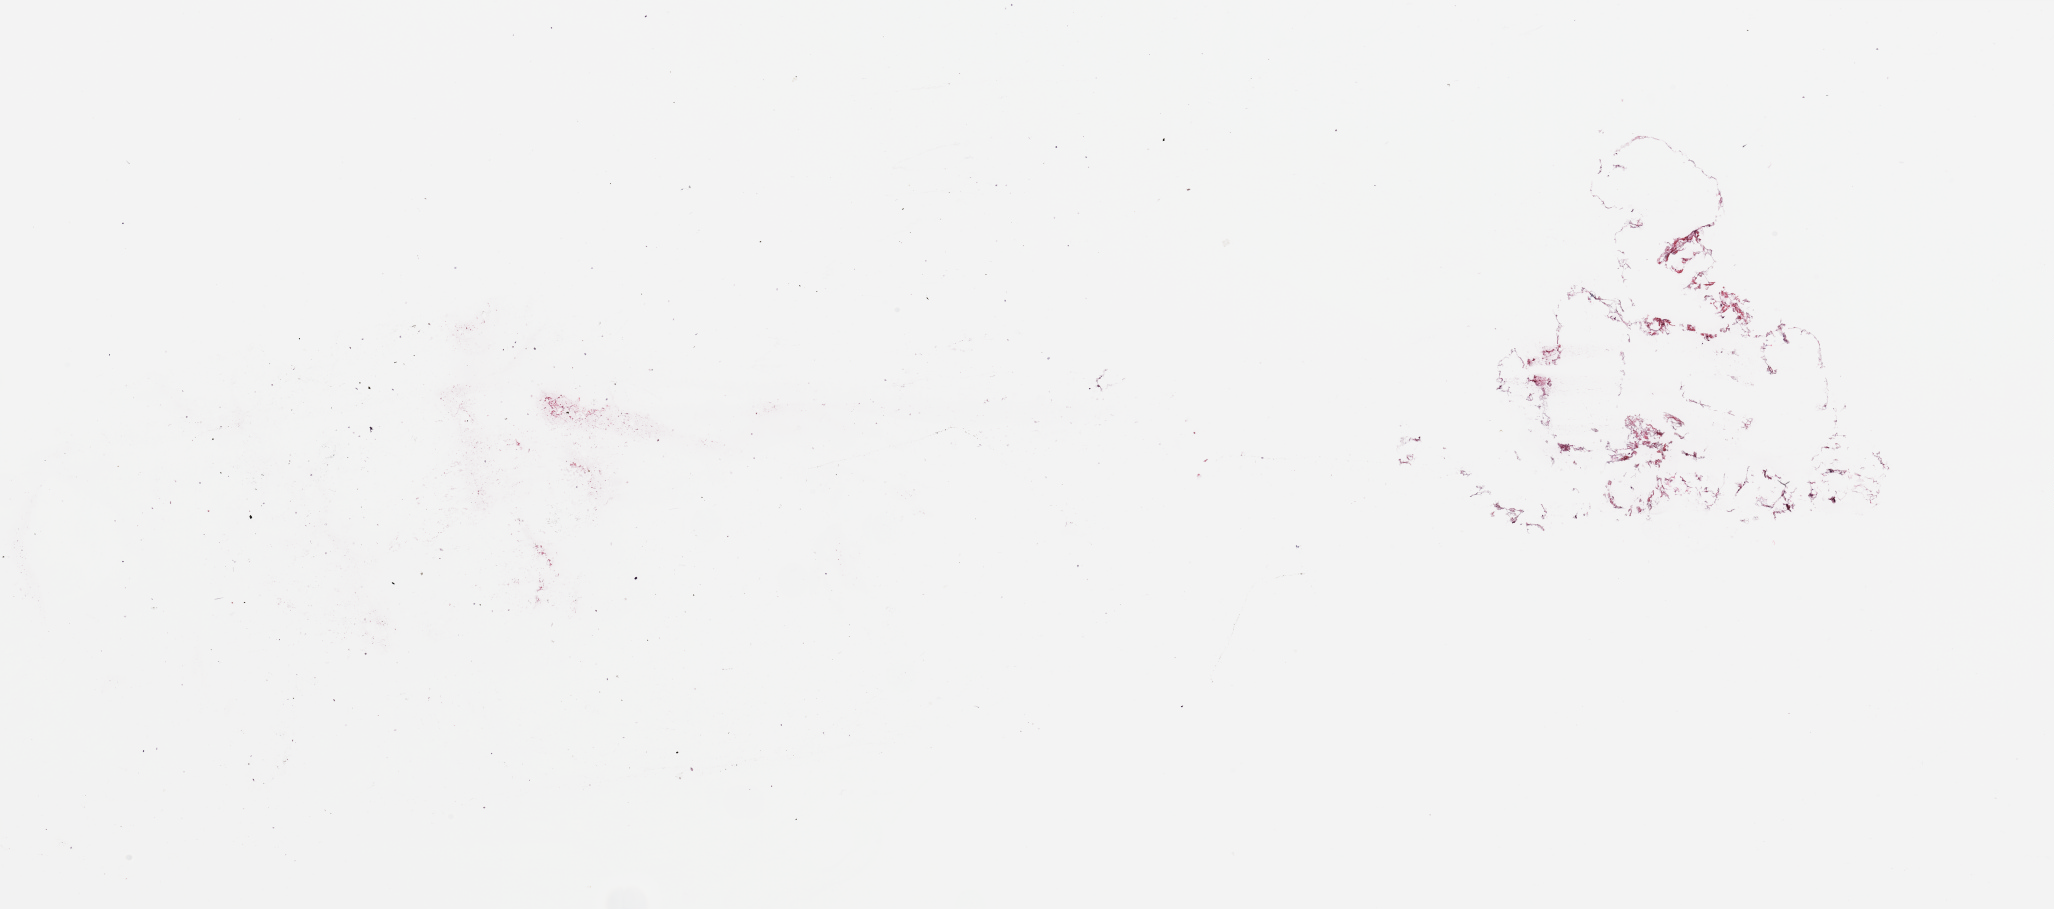
Whole-slide histology image, Hematoxylin and eosin (H&E) stained, low-resolution overview of the scanned area, about 32.5 x 14.4 mm (slide scanned at 20x). Tumour tissue sample, breast. Female, 59 y/o.
• diagnosis: Adenocarcinoma, NOS
• AJCC pathologic stage: II